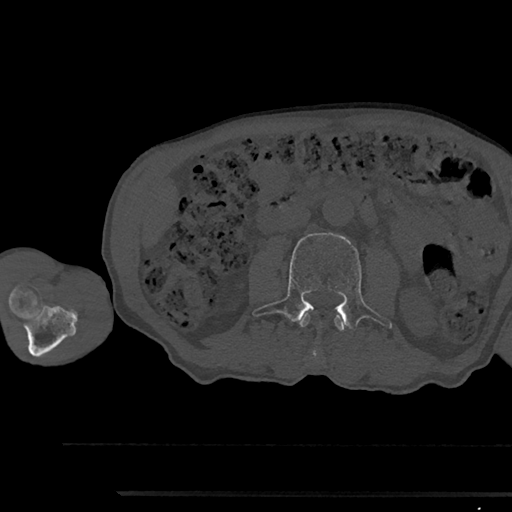
CT including the spine, one axial slice; position 504 of 797 along the scan axis; 120 kVp; bone window (W 1800 / L 400 HU); 0.5 mm slice thickness; 512 × 512 image matrix, field of view 367 × 367 mm. Male patient, age 79 years. From the clinical record (not read from this slice): primary cancer: prostate.
Structures marked on this image (semi-automatic segmentation, software-assisted and operator-edited):
- L2 vertebra: bounding box <299,315,345,331> (left, top, right, bottom; pixels)
- L3 vertebra: <252,233,393,356>